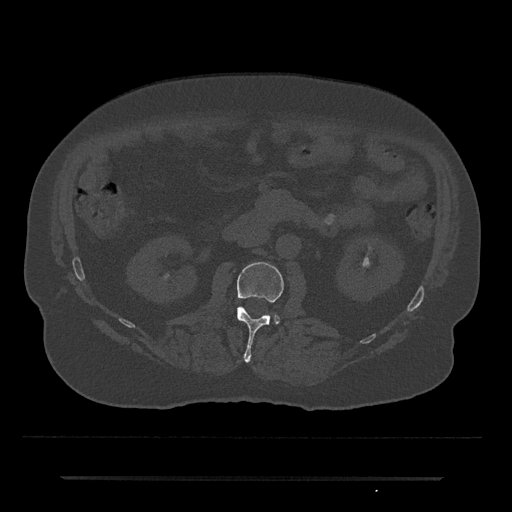
CT including the spine, one axial slice. Position 3 of 797 along the scan axis. Reconstruction kernel Br40s/3. 120 kVp. Bone window (W 1800 / L 400 HU). 0.5 mm slice thickness. 512 × 512 image matrix, field of view 437 × 437 mm. Patient: male, 69 years. Case-level facts recorded for this patient, not image findings: primary cancer: prostate.
Structures marked on this image (semi-automatically segmented with operator editing):
- L2 vertebra: bounding box (x1, y1, x2, y2) in pixels: (237, 262, 284, 362)